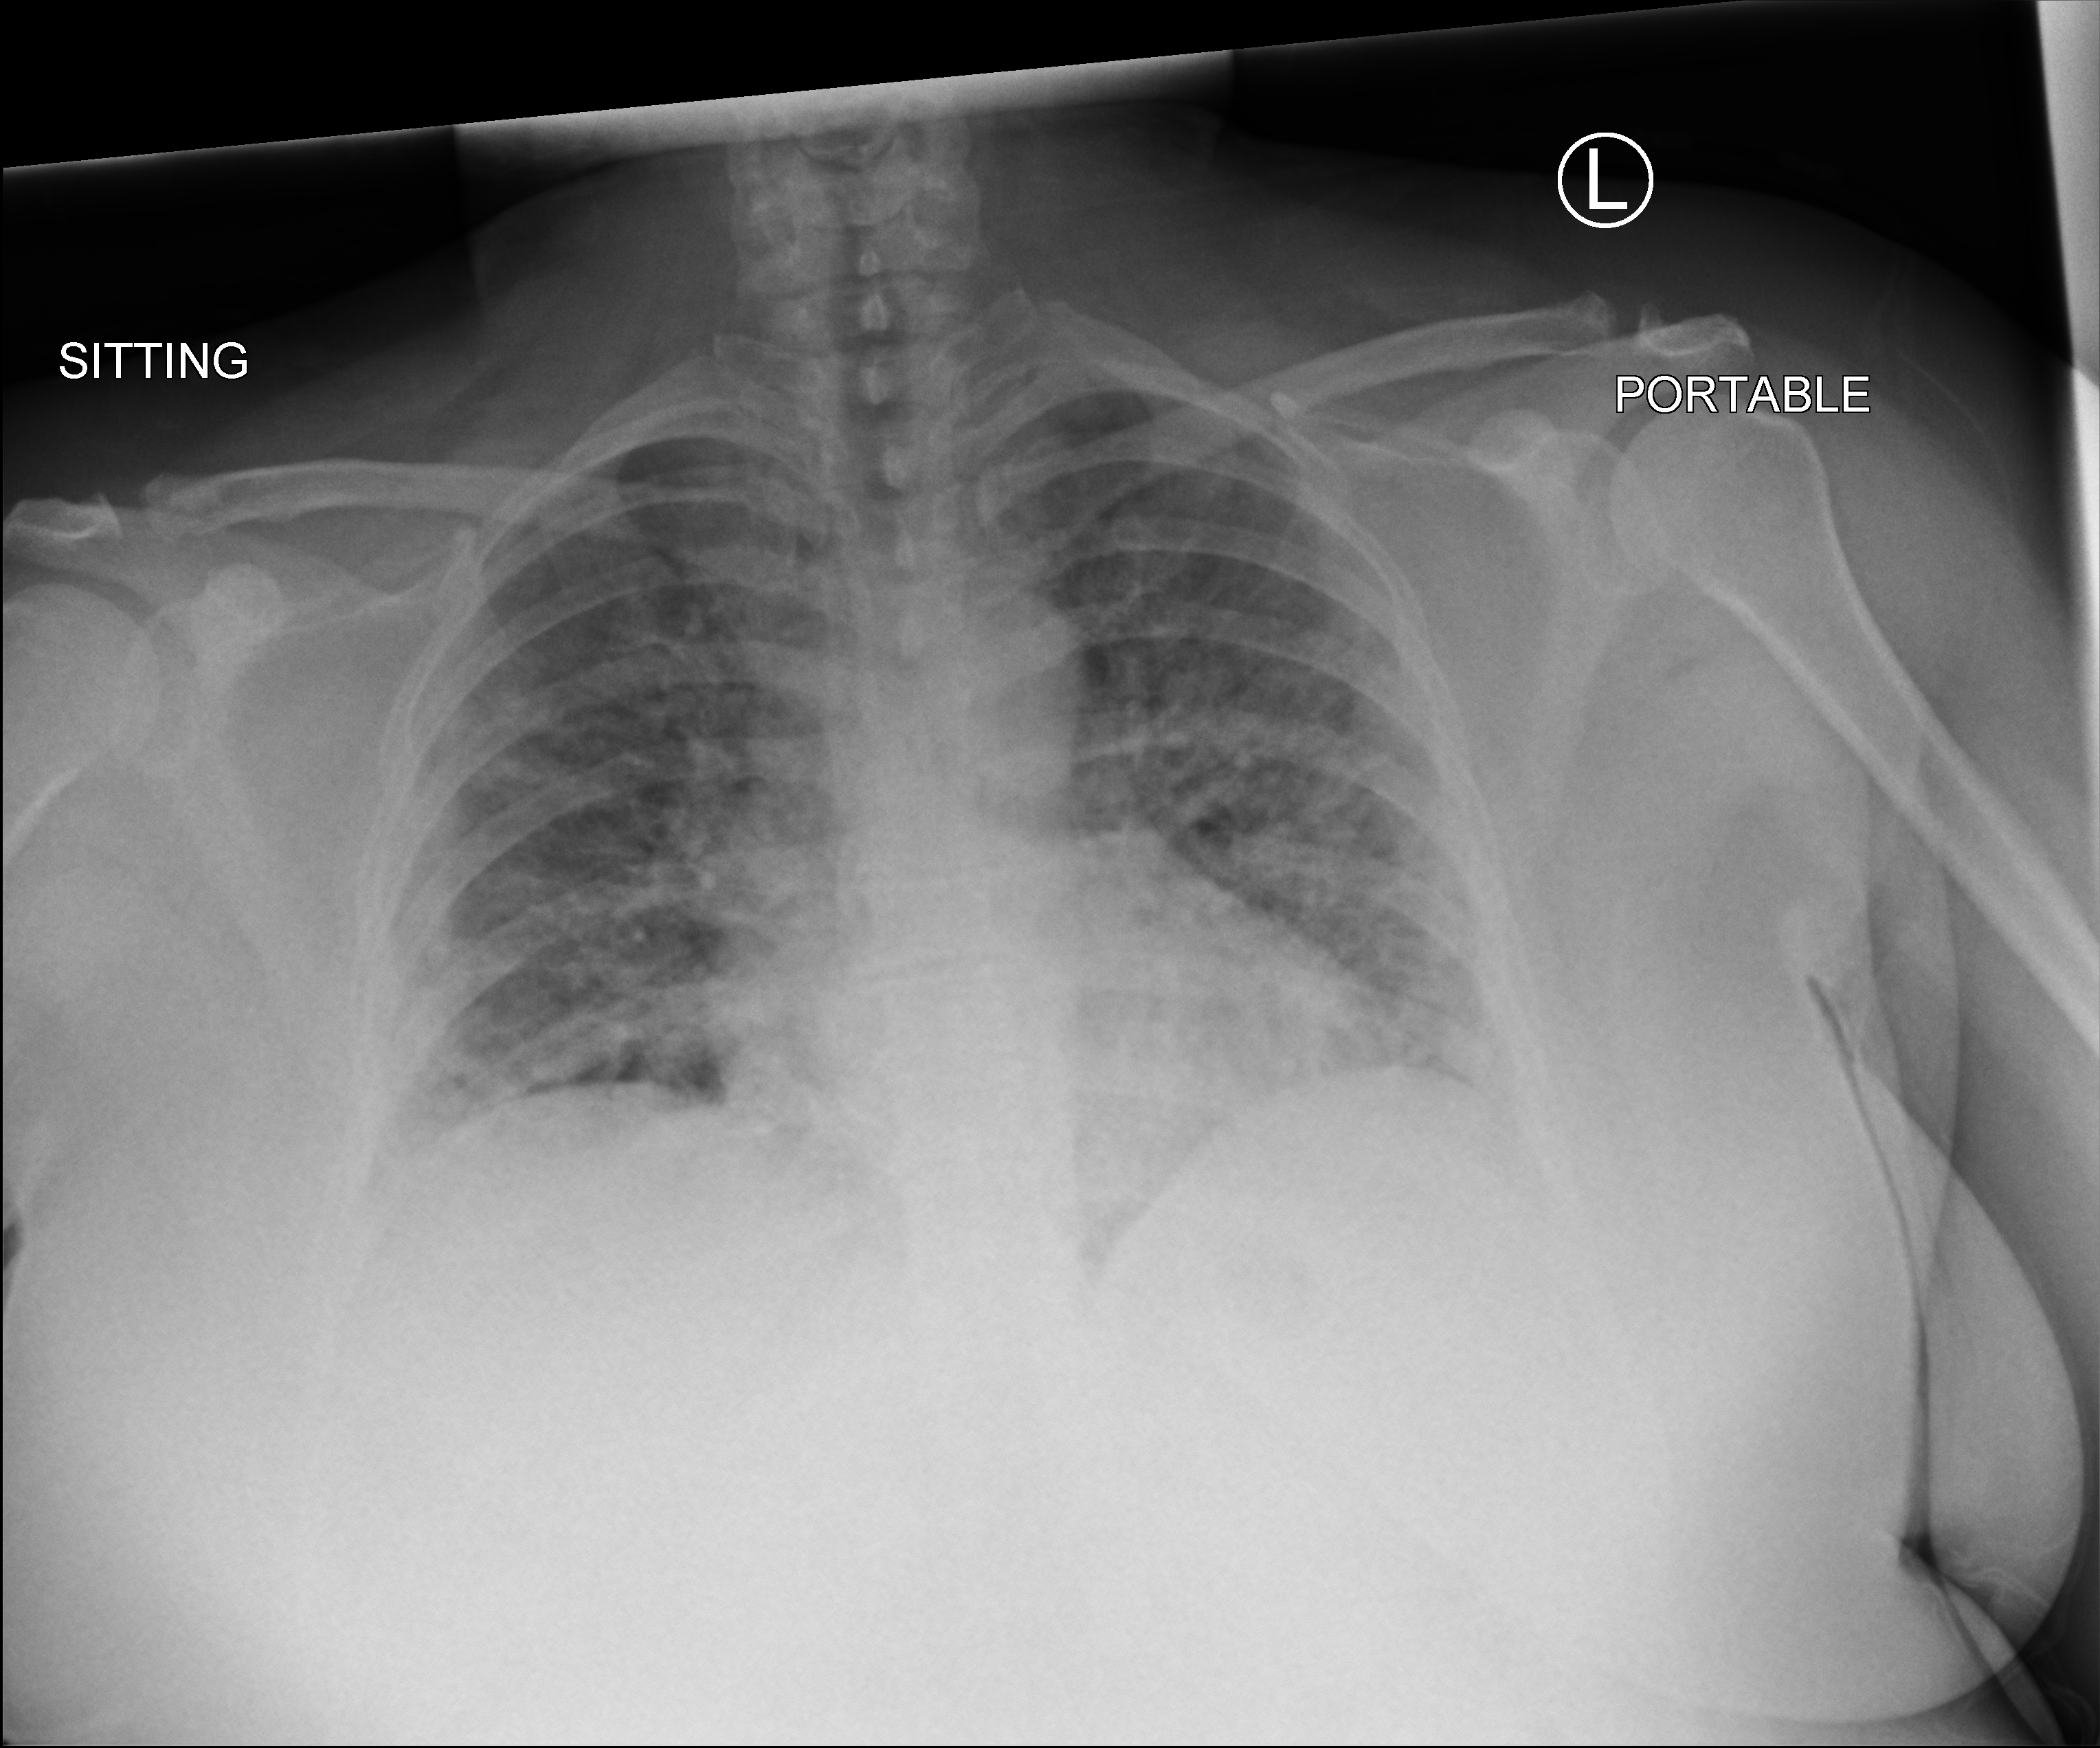
Bedside chest radiograph (computed radiography); anteroposterior (AP) projection. Patient hospitalised with COVID-19; female, aged 18–59 years.
From the hospital-stay record, not from the radiograph (when in the stay this image was taken is not recorded):
- mechanically ventilated during this hospital stay: yes
- admitted to intensive care during this hospital stay: yes
- hypertension (admission record): yes